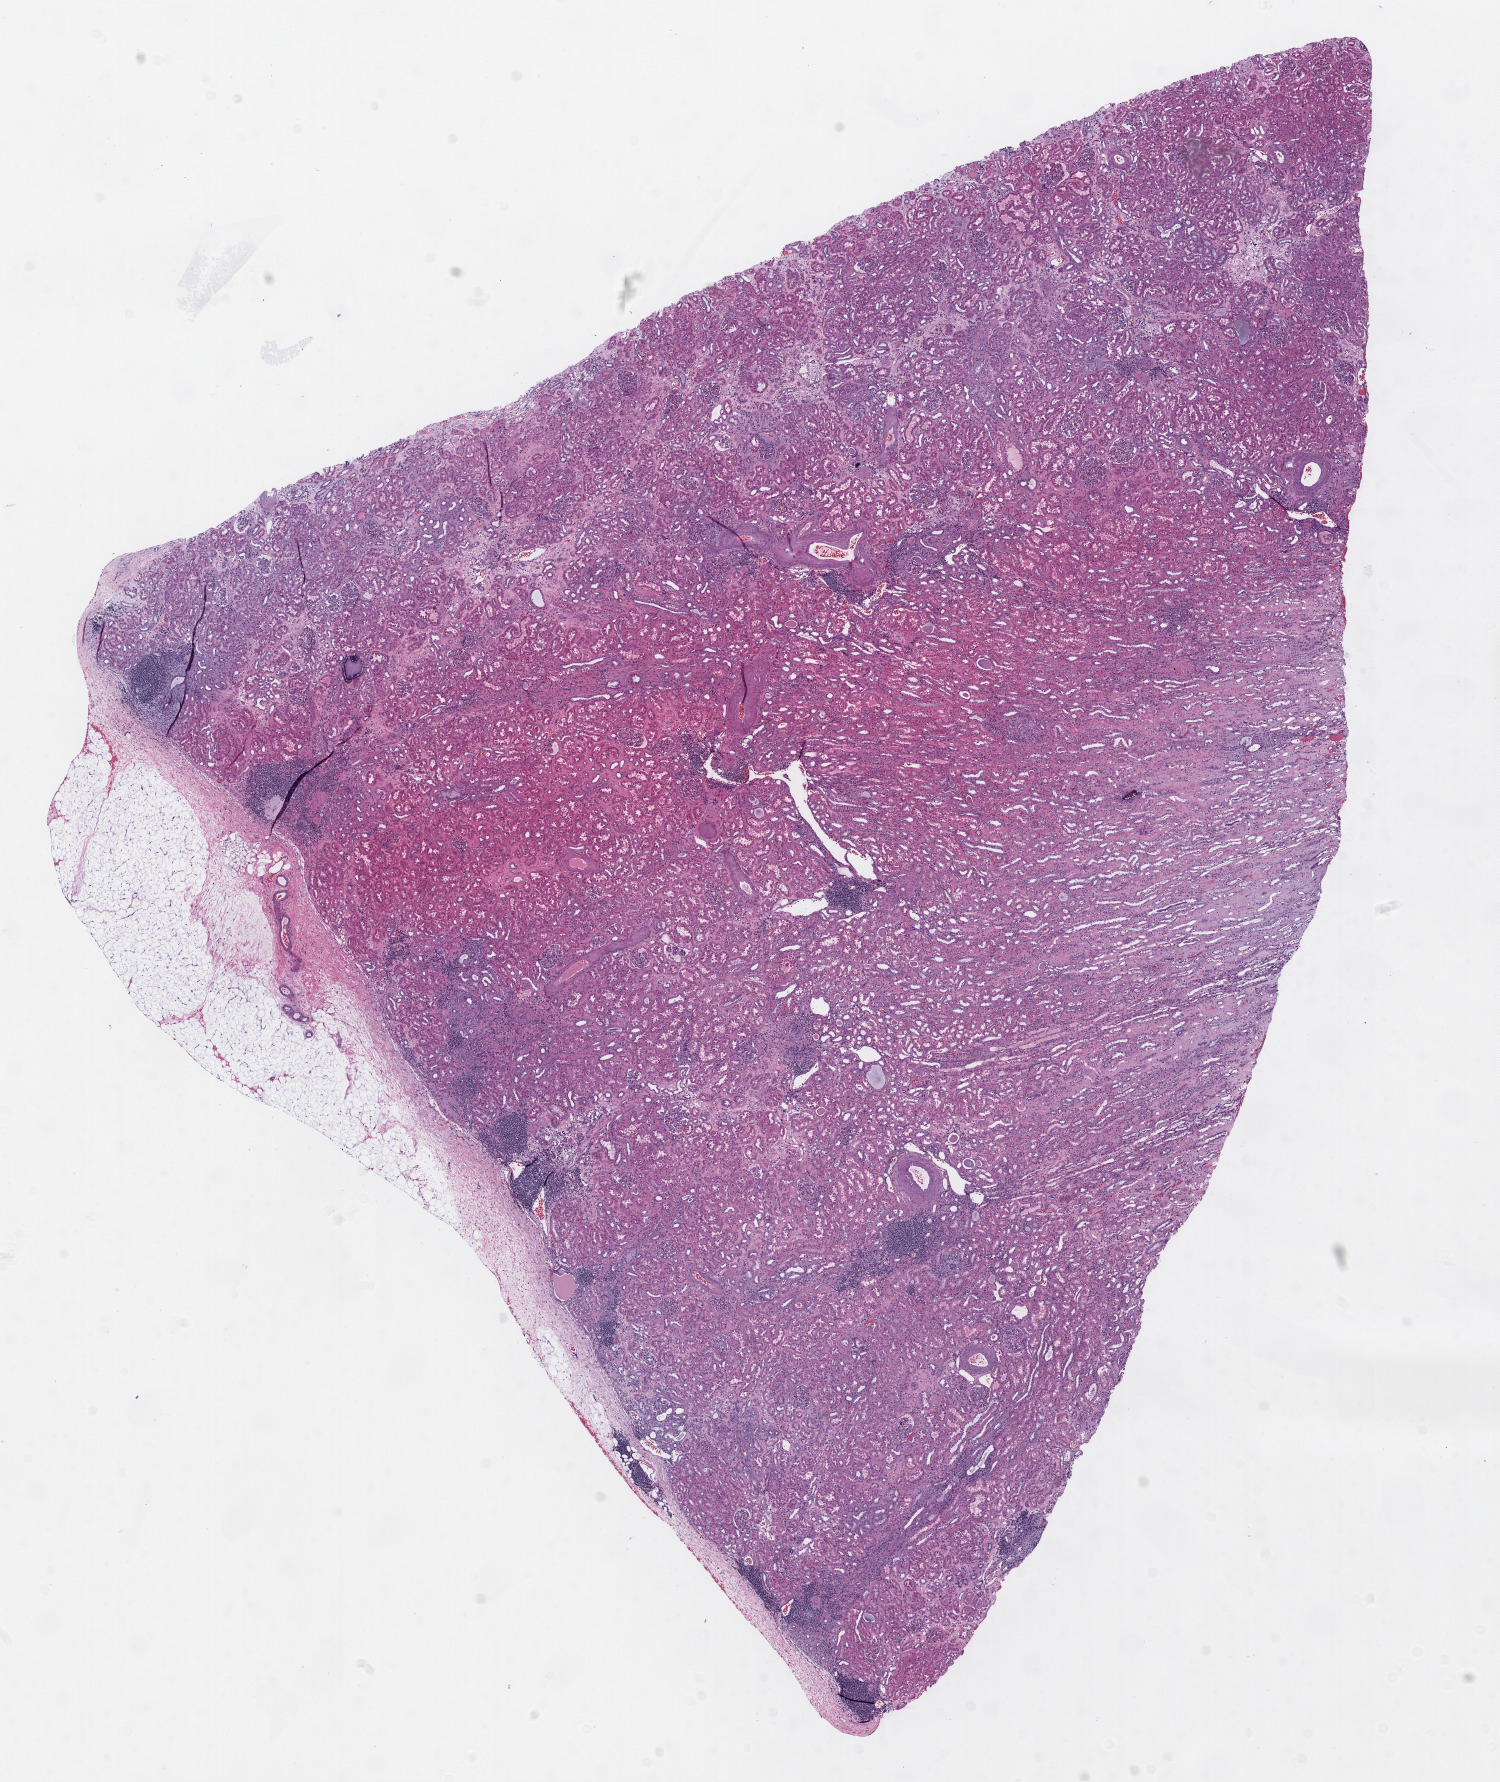
H&E whole-slide image, low-resolution overview of the scanned area, about 12.0 x 14.3 mm (slide scanned at 20x); frozen section; kidney, solid tissue normal (non-tumour tissue) sample. Male, age 73 years at initial diagnosis.
This section: solid tissue normal sample (biorepository sample class). Patient diagnosis: Clear cell adenocarcinoma, NOS.